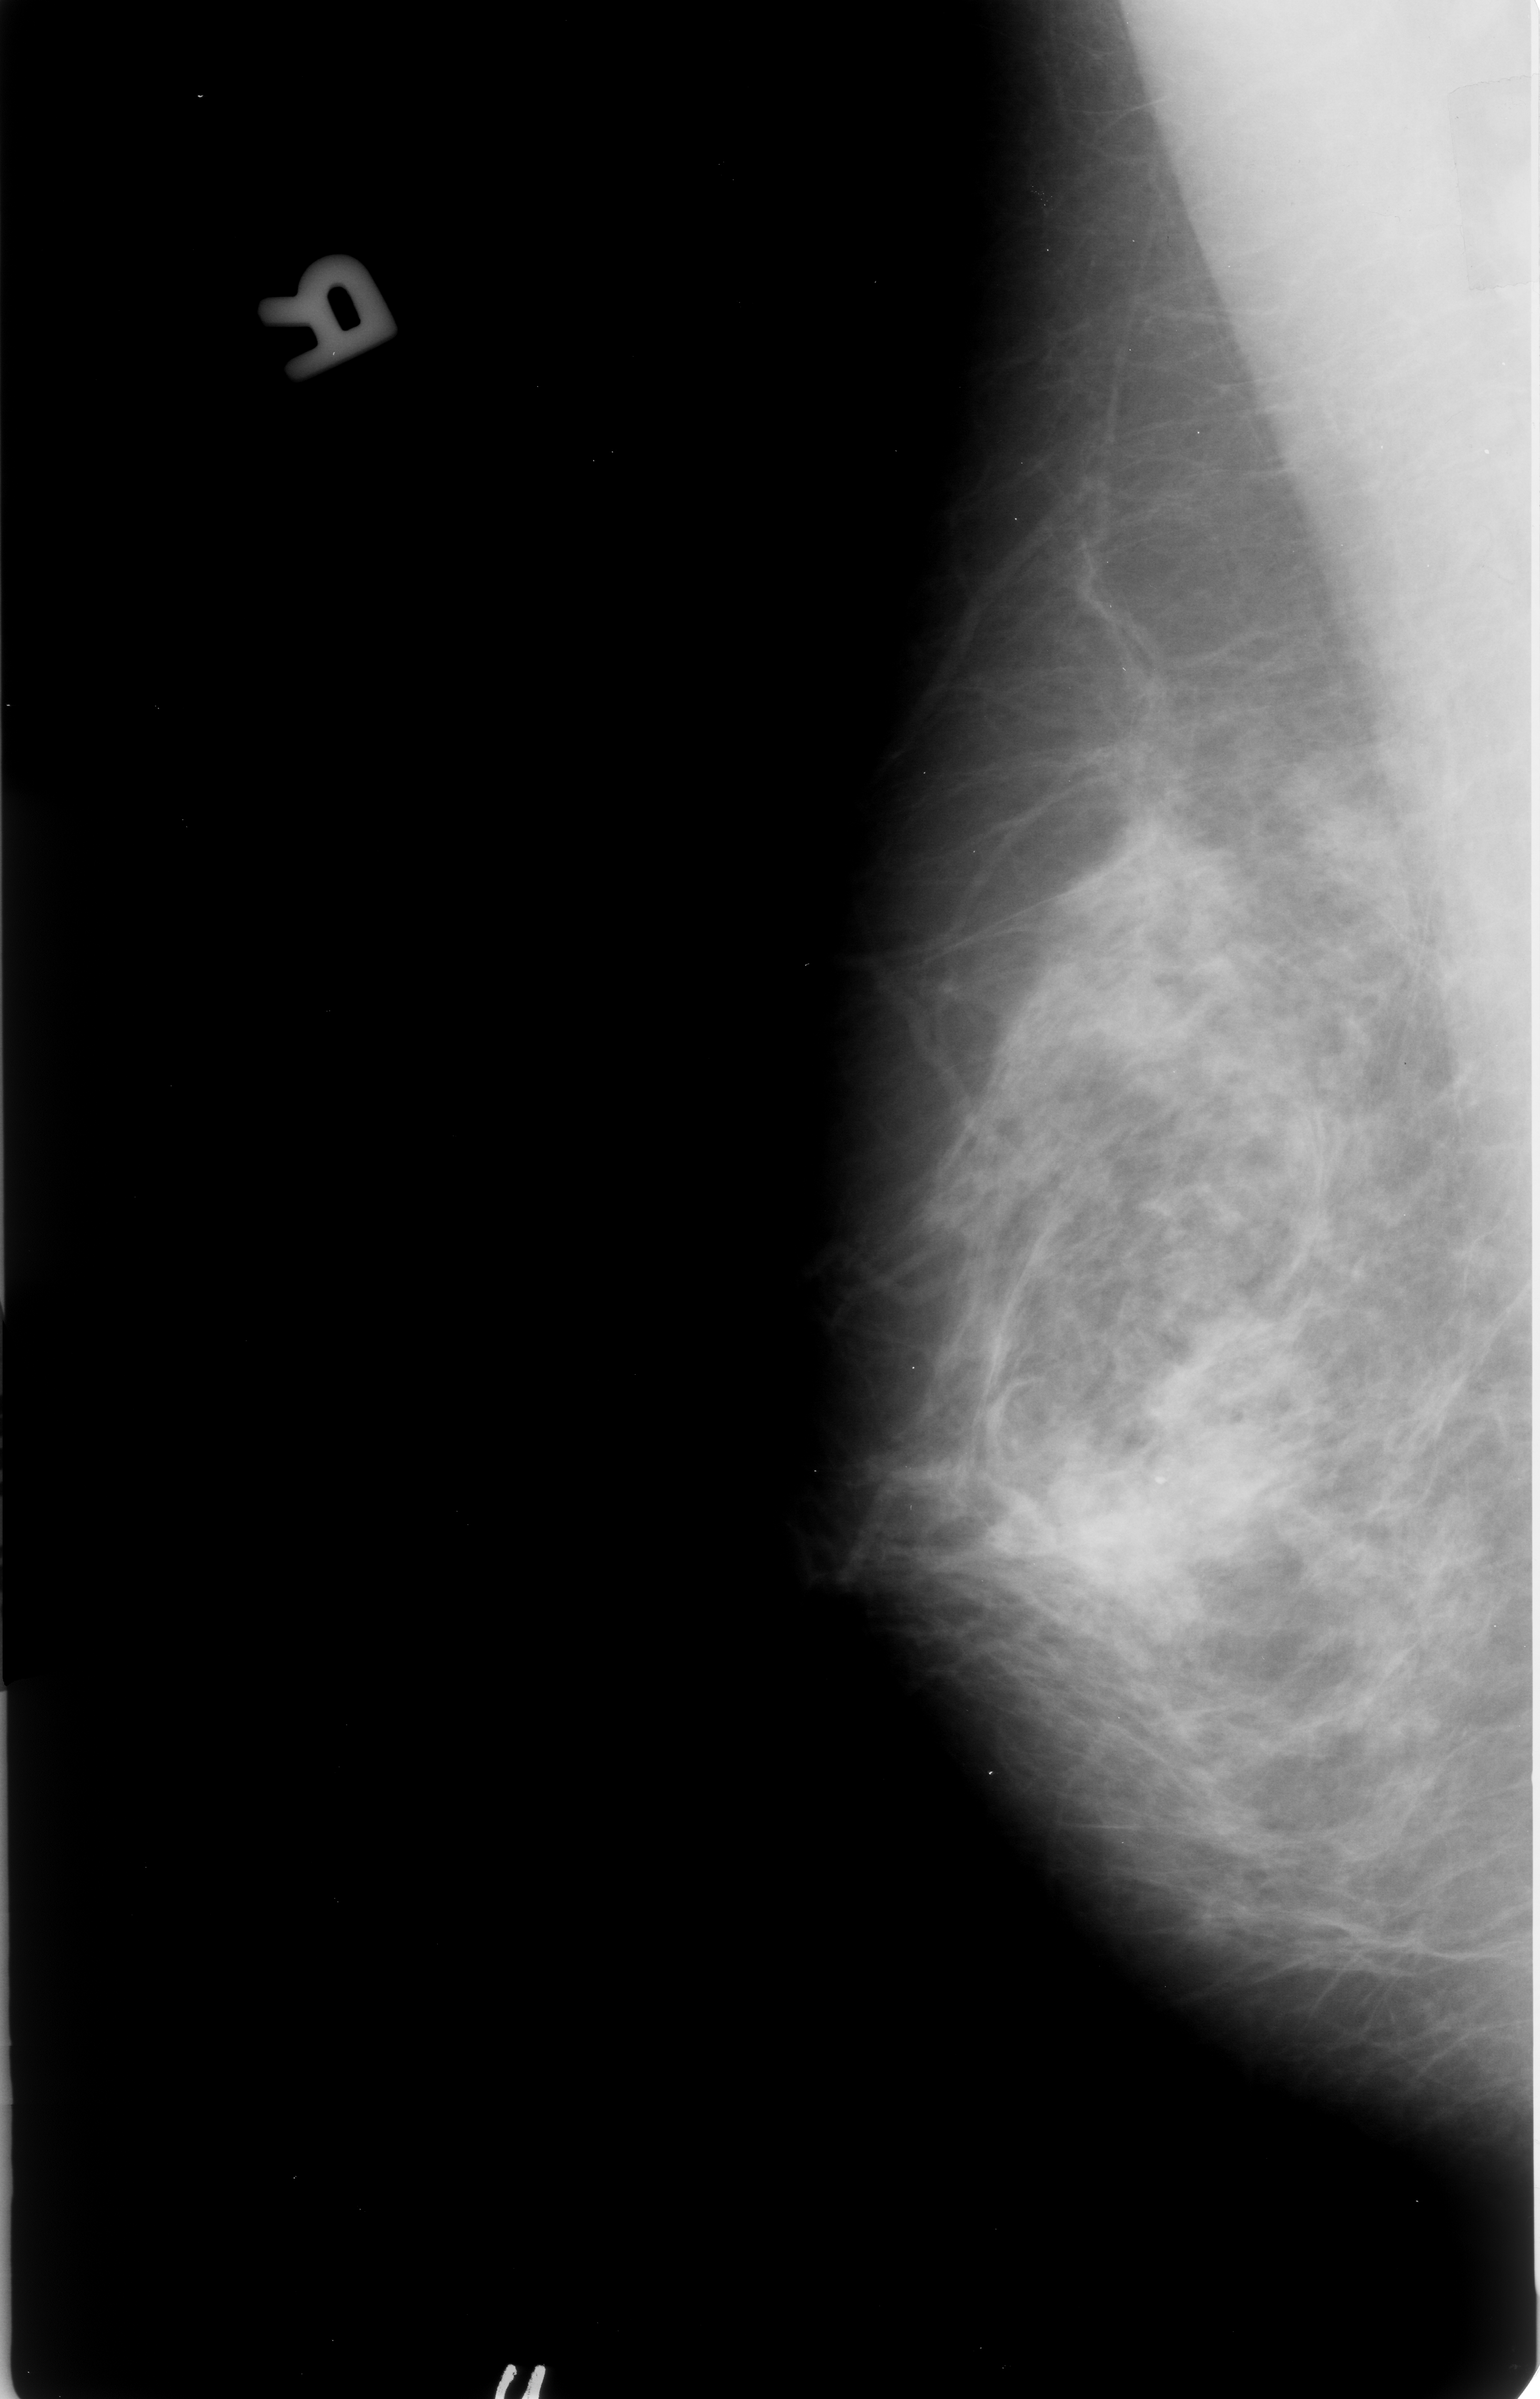
Digitized screen-film mammogram; right breast; MLO view; 1540 × 2399 image matrix.
Expert-marked regions of interest on this image (one box per marked abnormality):
- calcifications, morphology pleomorphic, distribution clustered; BI-RADS assessment category 3; pathology (as recorded): malignant: bounding box (x1, y1, x2, y2) in pixels: (959, 1275, 1343, 1655)